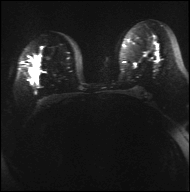
Breast MRI, one axial slice; slice 20 of 42 in the series (ordered by position); diffusion-weighted series; image 2 of 4 stored at this slice position (different b-values; order by instance number); 3 T; 4 mm slice thickness; 190 × 192 image matrix. Female patient.
Structures marked on this image (manually delineated by an expert):
- tumour on diffusion-weighted imaging: bounding box <80,67,90,72> (left, top, right, bottom; pixels)